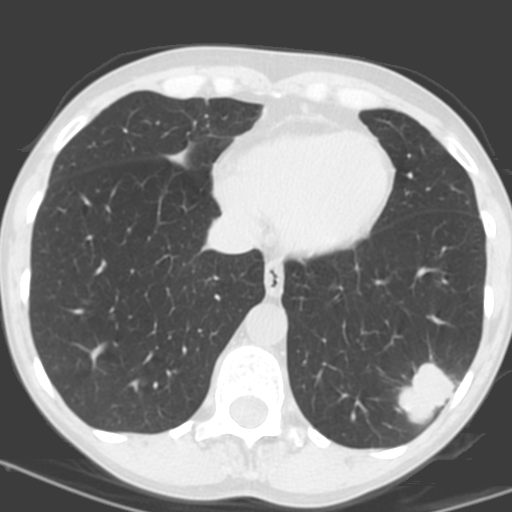
Axial slice from a low-dose chest CT screening exam; baseline annual screen; lung window (W 1500 / L -600 HU); 3.2 mm slice thickness; standard (soft-tissue) reconstruction kernel (C); slice 110 of 156 in the series; 512 × 512 image matrix, field of view 262 × 262 mm. Female participant, aged 56 years at enrolment. Current smoker at enrolment.
Lesion marked by an expert reader, bounding box (x1, y1, x2, y2) in pixels: (388, 358, 464, 427). The exam's reader record, not a measurement of the box and not confirmed to be the same lesion: non-calcified nodule or mass ≥4 mm, left lower lobe, 31 × 23 mm, poorly defined margins, soft tissue attenuation, pre-existing on the prior screen: no.